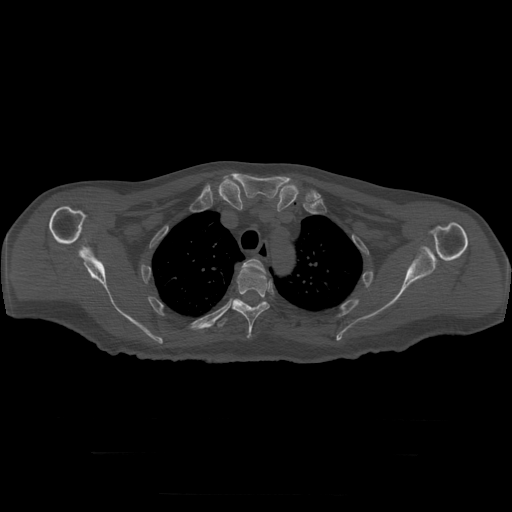
CT including the spine, one axial slice; slice 241 of 397 in the series (ordered by position); reconstruction kernel STANDARD; 120 kVp; bone window (W 1800 / L 400 HU); 1.25 mm slice thickness; 512 × 512 image matrix, field of view 510 × 510 mm. Patient age 73 years. Case-level facts recorded for this patient, not image findings: primary cancer: prostate.
Outlined on this slice (semi-automatic segmentation, software-assisted and operator-edited):
- T3 vertebra: bounding box <244,259,265,274> (left, top, right, bottom; pixels)
- T4 vertebra: <232,268,270,339>
- T5 vertebra: <218,298,261,328>